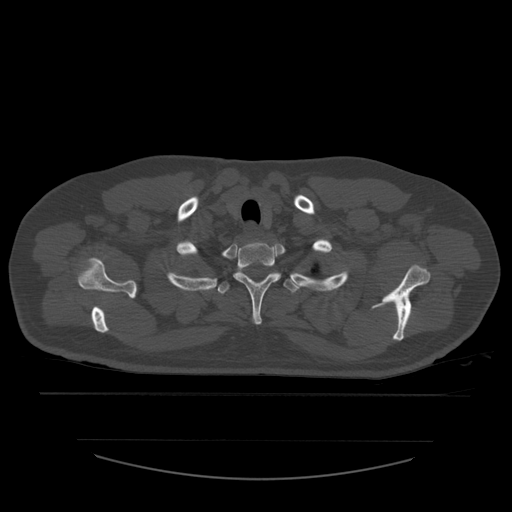
CT including the spine, one axial slice. Position 464 of 532 along the scan axis. Reconstruction kernel STANDARD. 120 kVp. Bone window (W 1800 / L 400 HU). 1.25 mm slice thickness. 512 × 512 image matrix, field of view 441 × 441 mm. Patient age 44 years. Case-level facts recorded for this patient, not image findings: primary cancer: soft tissue sarcoma.
Structures marked on this image (semi-automatically segmented with operator editing):
- T1 vertebra: bounding box (x1, y1, x2, y2) in pixels: (233, 242, 282, 325)
- T2 vertebra: (218, 272, 313, 294)